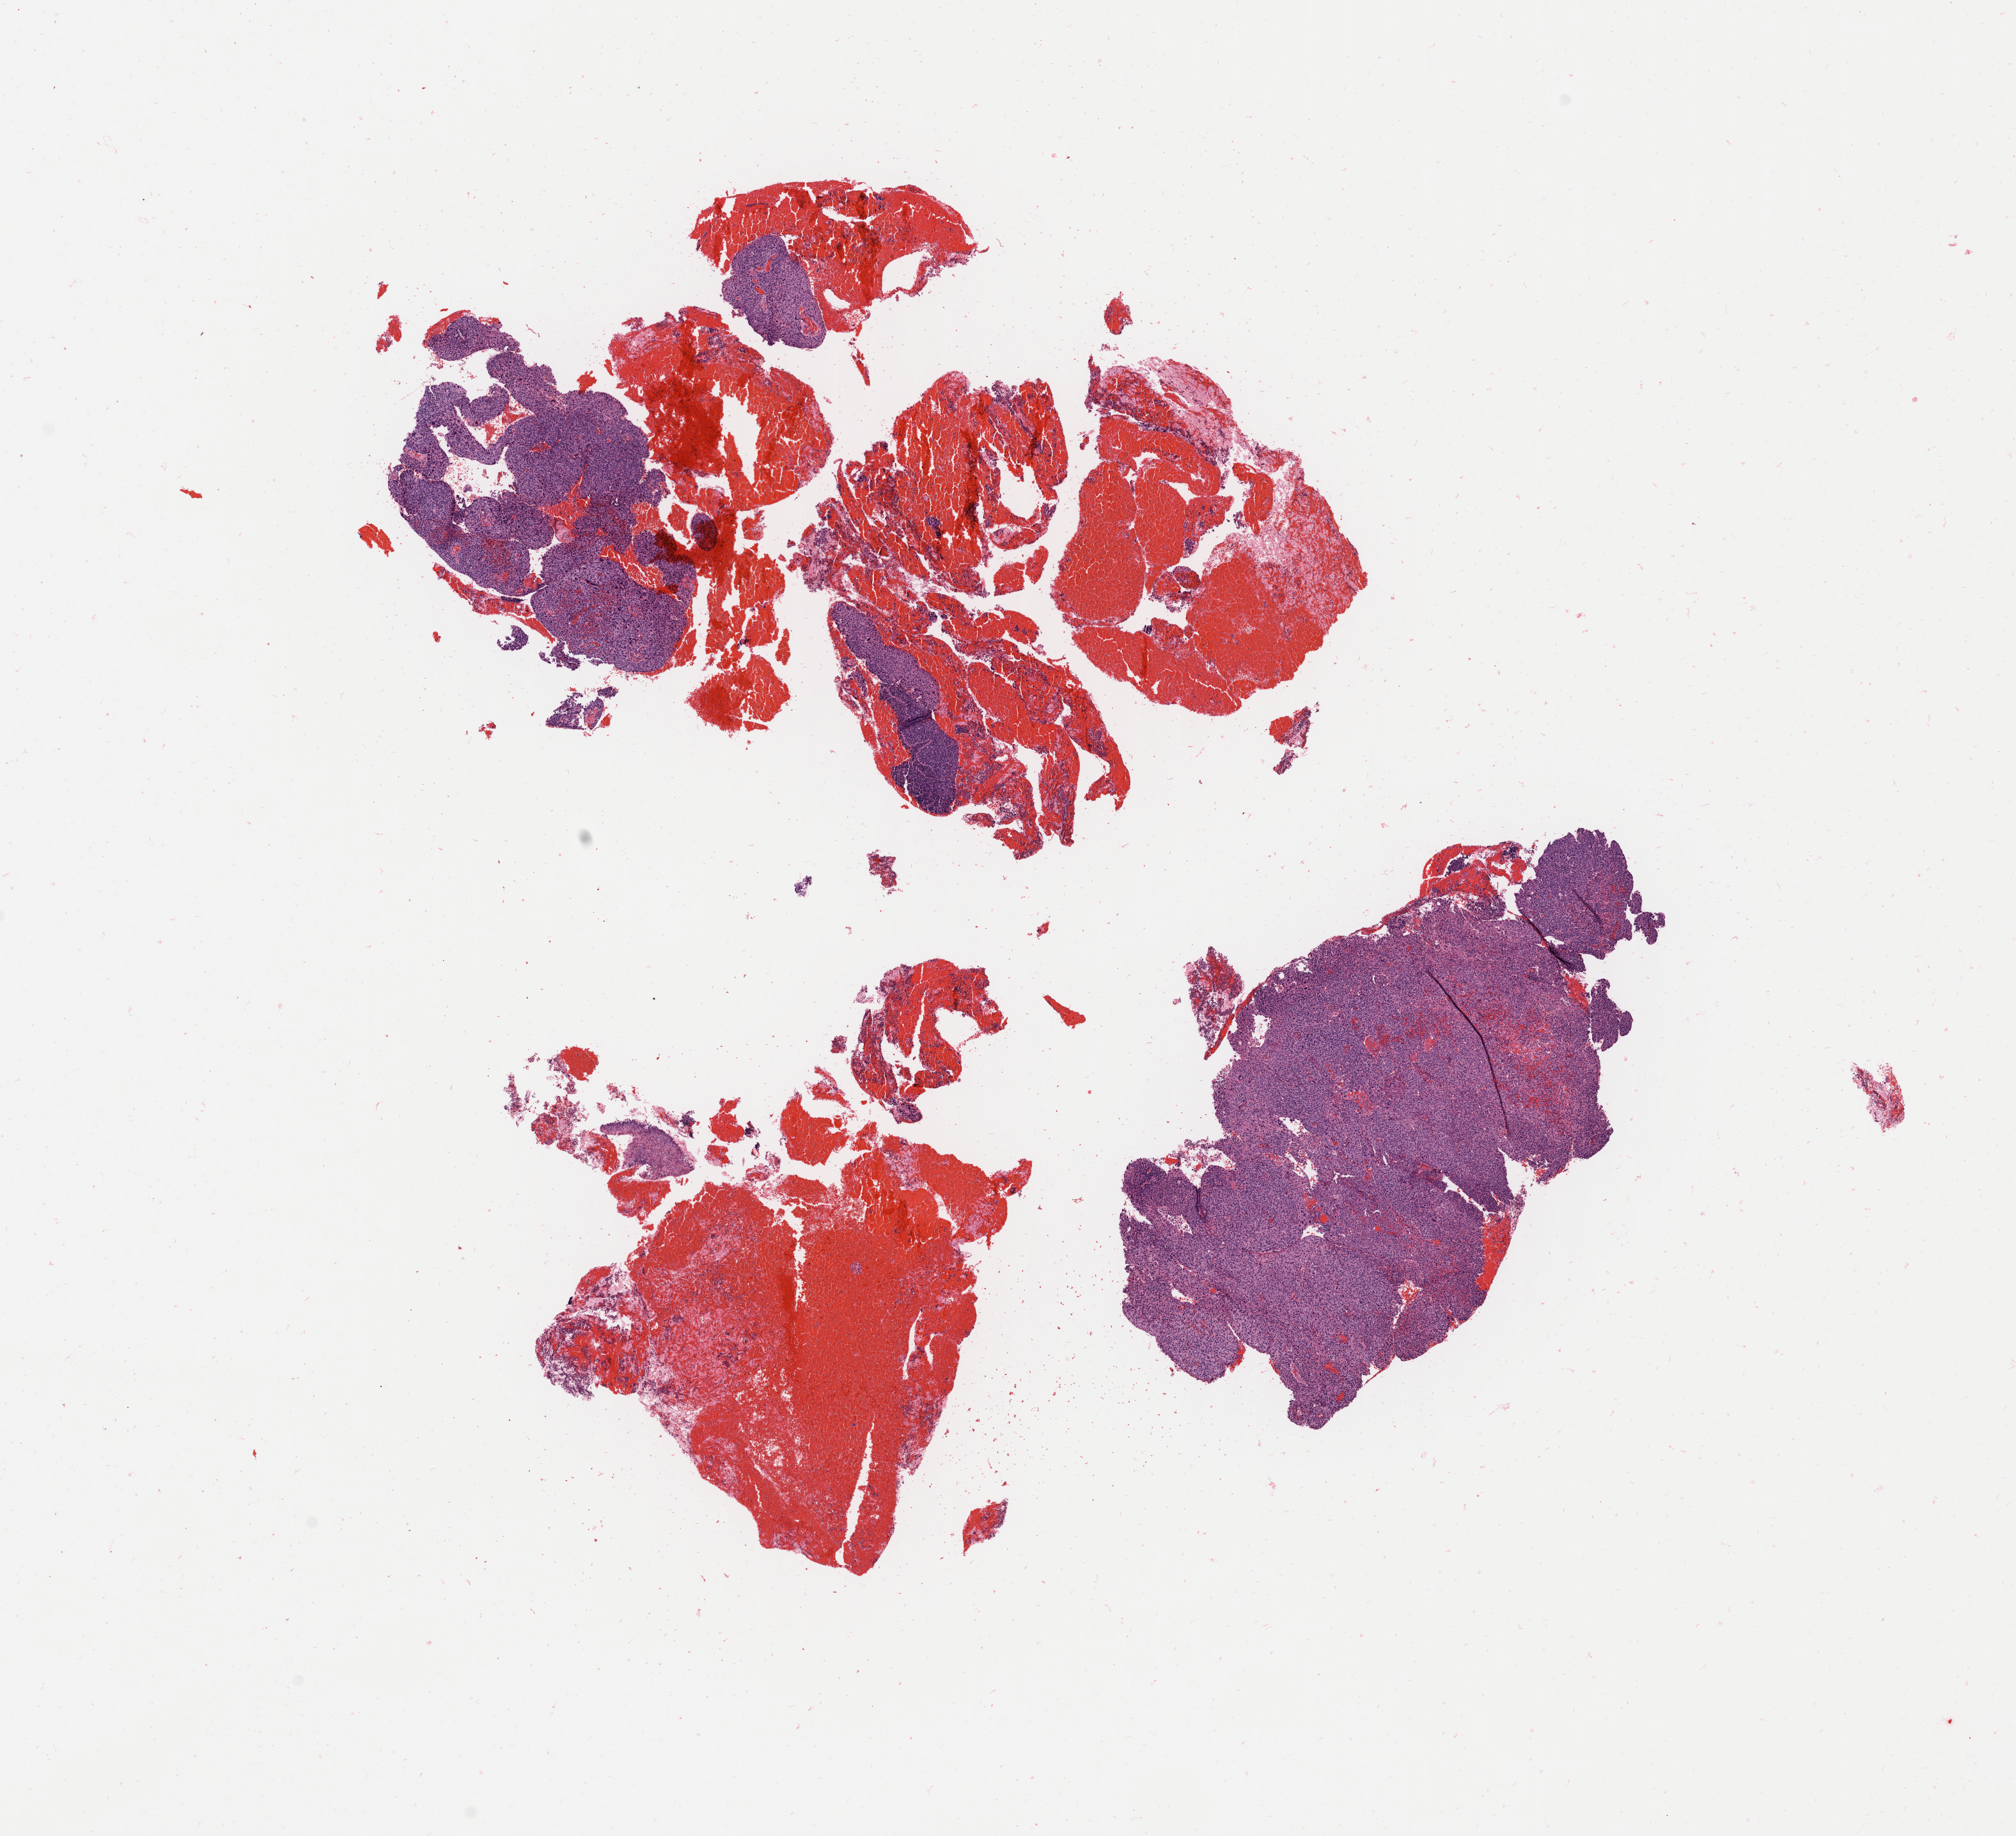
Whole-slide image, H&E stain — low-resolution overview of the scanned area, about 12.5 x 11.4 mm; tumor tissue; anatomic site: cervix. Patient: female, aged 59.
Histologic diagnosis: Squamous cell carcinoma, large cell, nonkeratinizing, NOS.